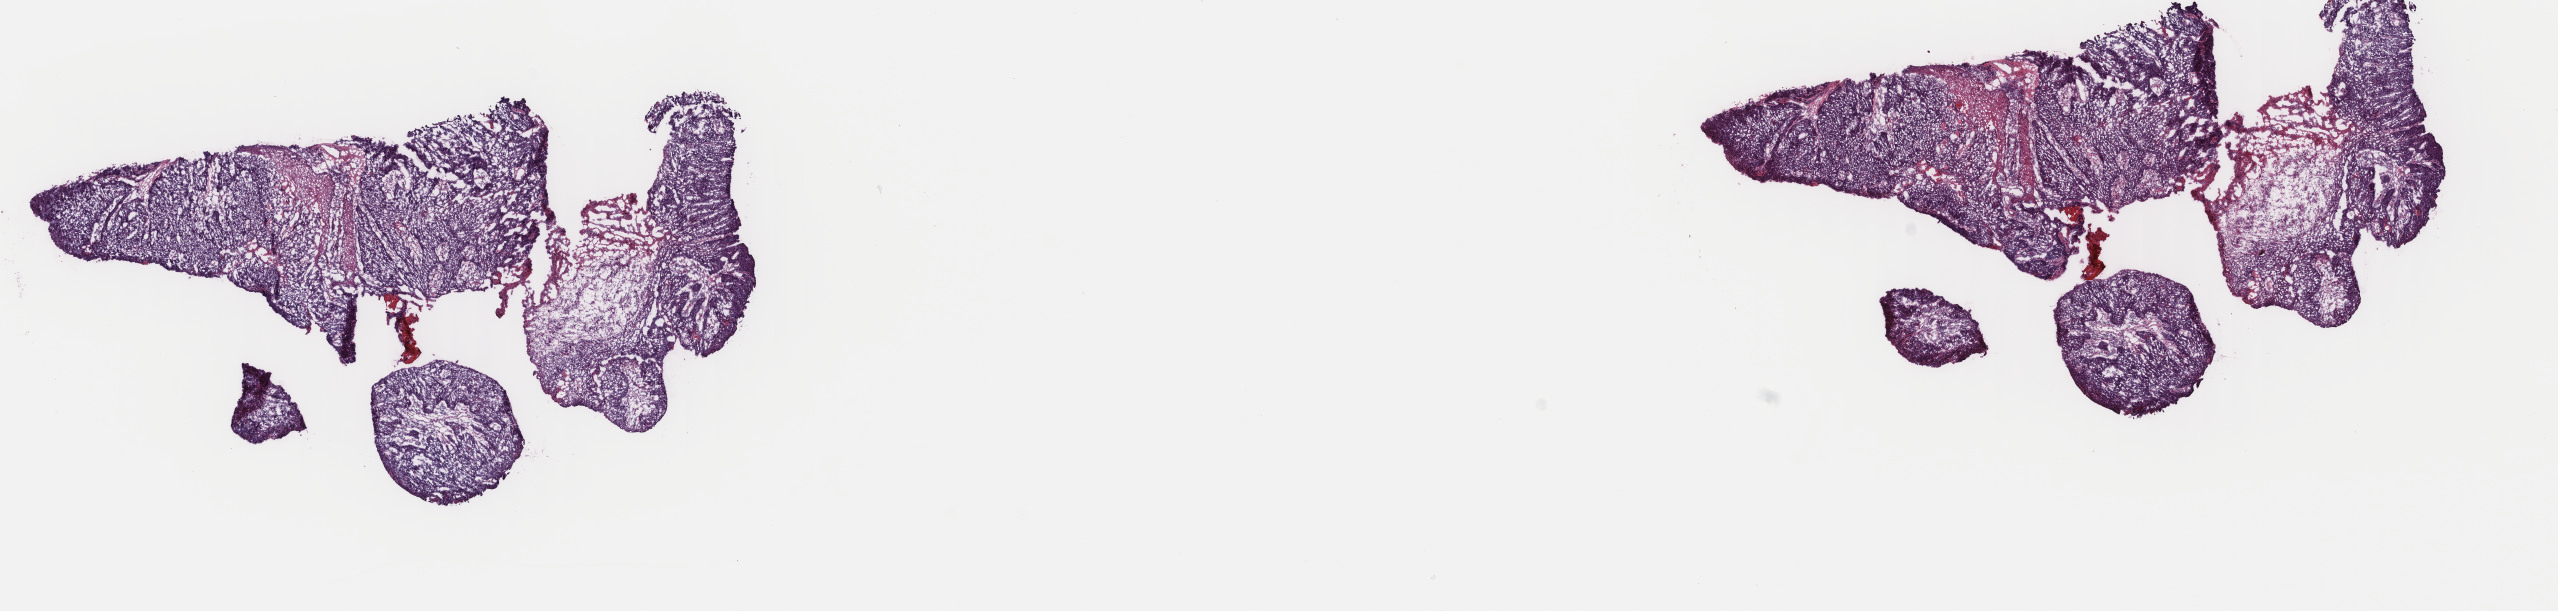
Whole-slide histology image, H&E-stained, whole scanned area (about 20.3 x 4.8 mm, slide scanned at 40x) shown as a low-resolution overview. Frozen section from the top of the tissue portion. Primary tumour sample from the head and neck. Patient: male, age at initial diagnosis 57 years. Histologic grade: G2 (moderately differentiated). Slide review estimates, as recorded: tumour cells 100%, tumour nuclei 75%, normal cells 0%, stromal cells 0%, necrosis 0%. Inflammatory infiltration, as recorded: lymphocyte infiltration 4%, monocyte infiltration 0%, neutrophil infiltration 0%.
- AJCC pathologic stage: IVA (7th edition)
- histologic diagnosis: Squamous cell carcinoma, large cell, nonkeratinizing, NOS (base of tongue, NOS)